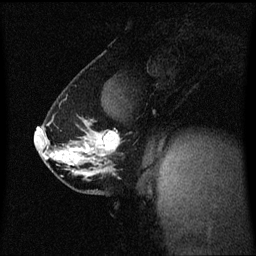
Breast MRI (dynamic contrast-enhanced), one sagittal slice; slice 37 of 60 in the series (ordered by position); dynamic contrast-enhanced series, image 2 of 3 at this slice position (ordered by acquisition); 1.5 T; TE 4.2 ms, TR 8.4 ms; 2 mm slice thickness; 256 × 256 image matrix, field of view 210 × 210 mm. Female patient, age 40 years. Case-level facts recorded for this patient, not image findings: setting: breast cancer imaged before/during neoadjuvant chemotherapy; receptor status: triple-negative.
Structures marked on this image (semi-automatically segmented with operator editing):
- analysis volume of interest (the breast-tissue region the enhancement analysis was run in; not a lesion): box from (x=35, y=118) to (x=123, y=188) px
- tumour enhancement mask (voxels above the 70 % enhancement threshold inside the analysis volume of interest): (x=36, y=128)–(x=121, y=163)